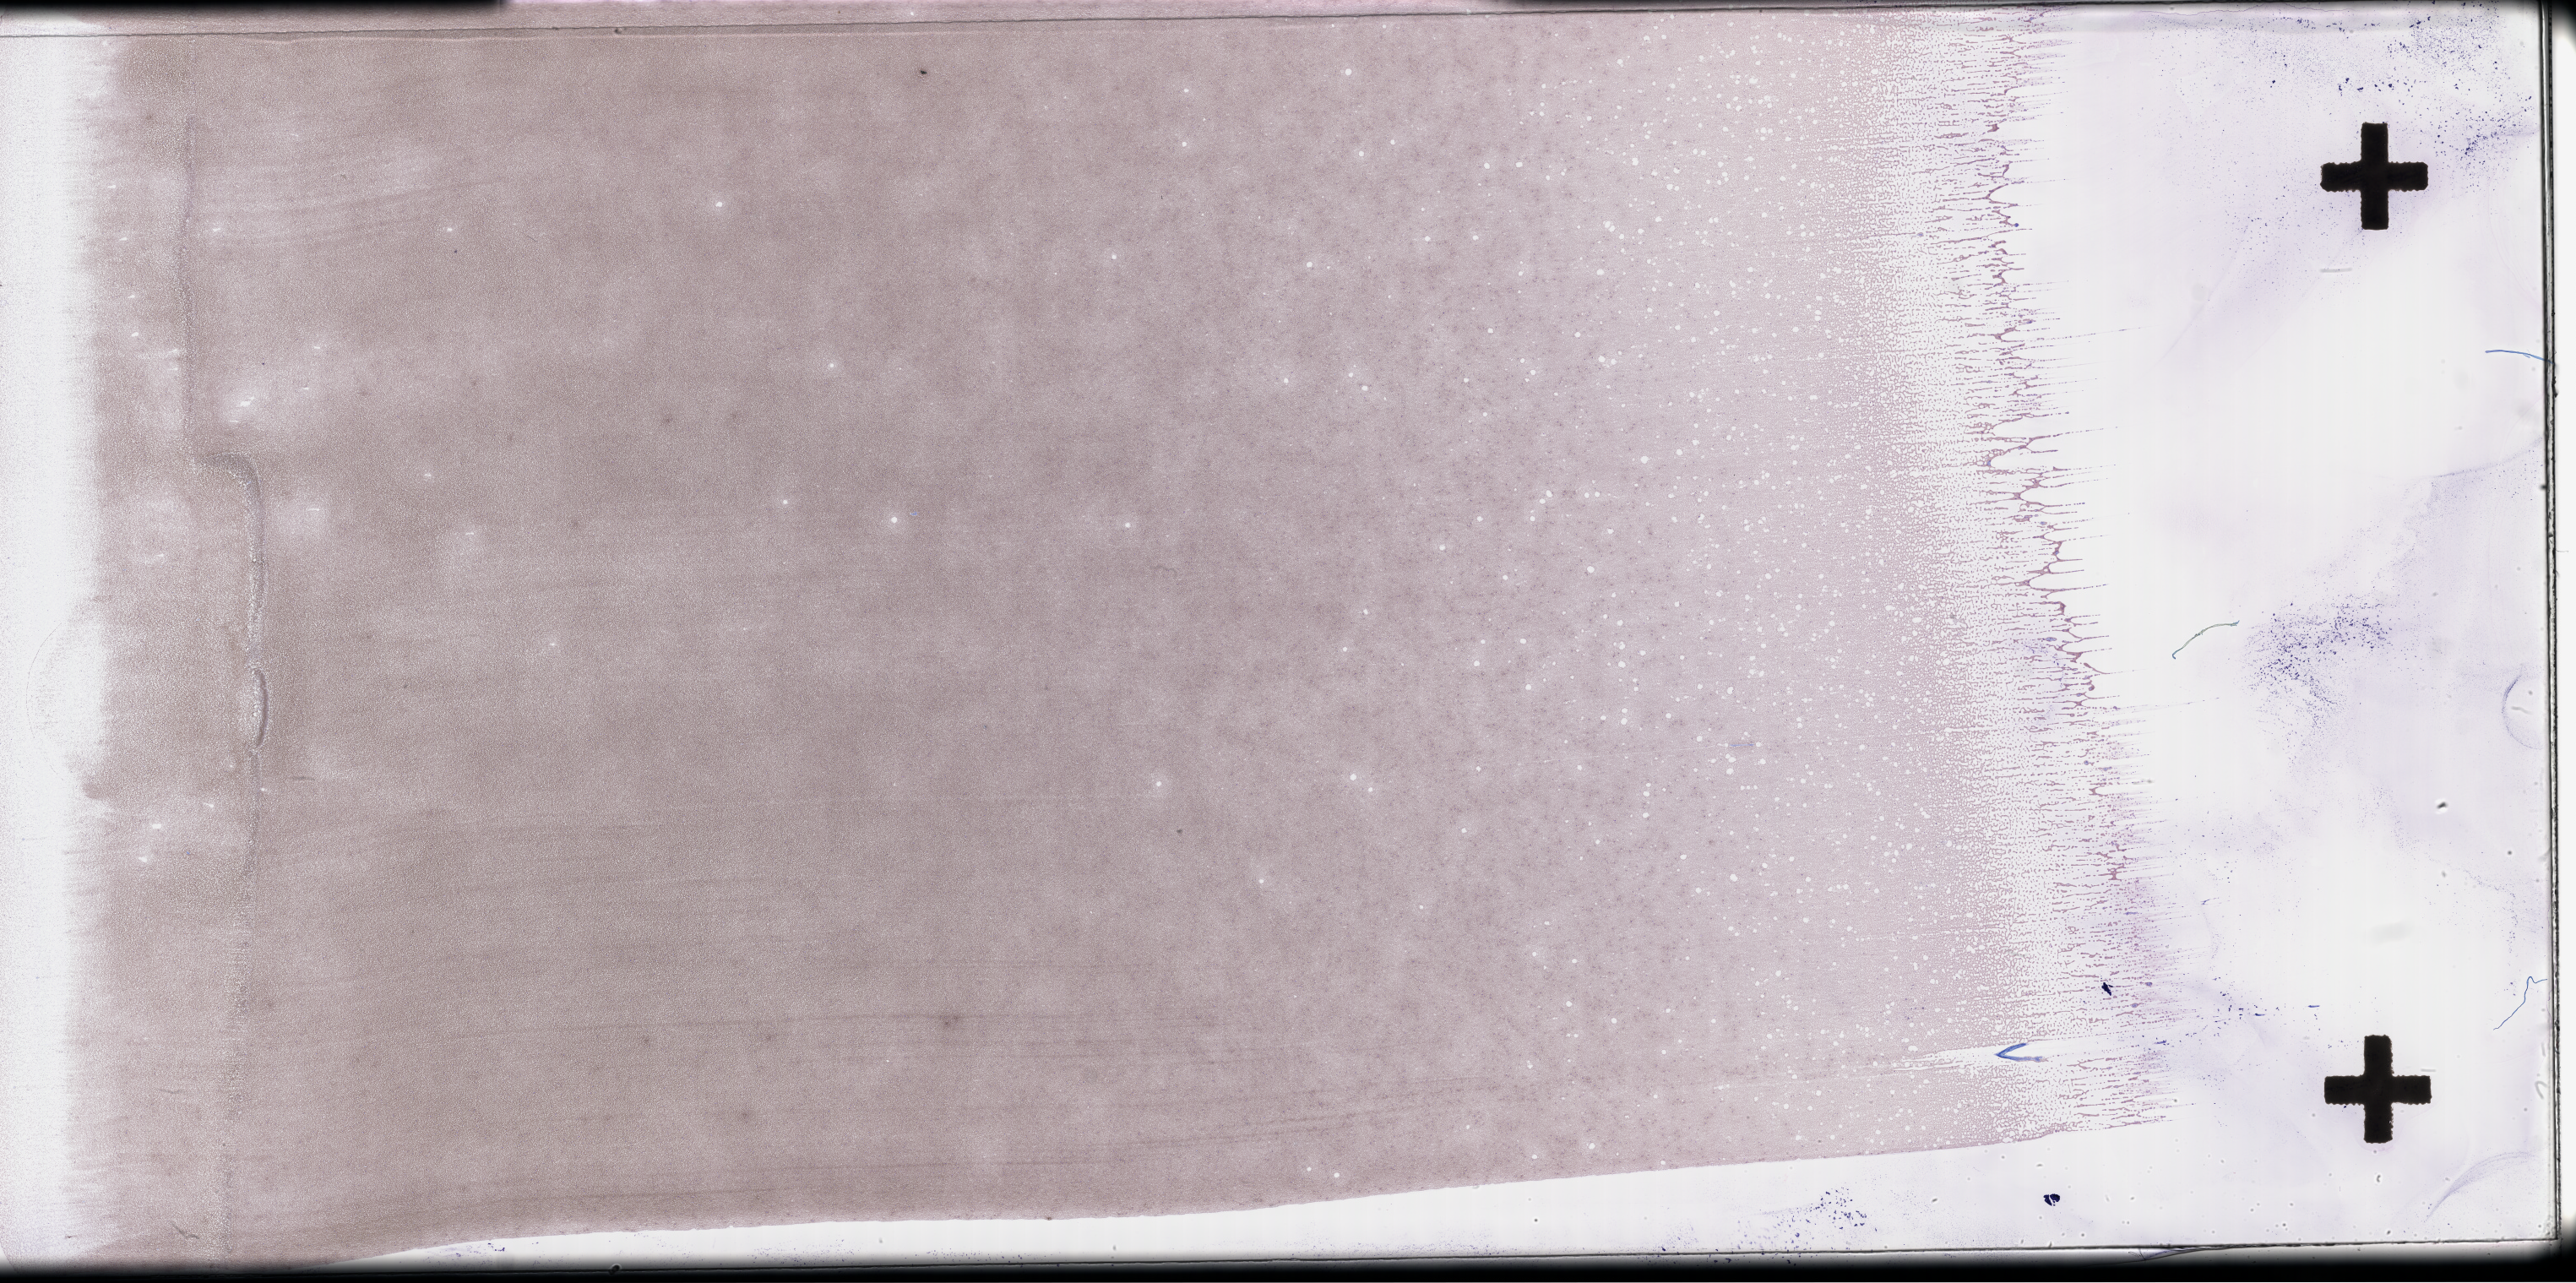
Wright-Giemsa-stained whole blood smear, whole-slide image, low-resolution overview of the scanned area, about 49.3 x 24.5 mm, smear from an EDTA sample. Male patient.
- from a patient with: Plasma Cell Myeloma